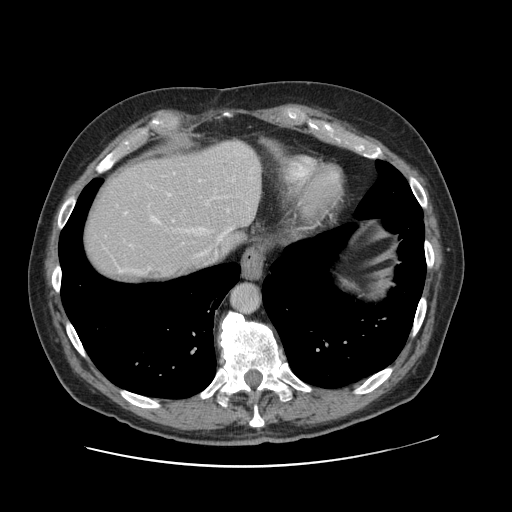
Contrast-enhanced abdominal CT, one axial slice; position 101 of 138 along the scan axis; 120 kVp; intravenous contrast given; soft-tissue window (W 400 / L 40 HU); 2.5 mm slice thickness; 512 × 512 image matrix, field of view 402 × 402 mm. Male patient, age 71 years. Case-level facts recorded for this patient, not image findings: diagnosis: colorectal cancer liver metastases, imaged before liver resection; multiple liver metastases: no; largest metastasis: 3.3 cm; disease in both lobes: no.
Annotated regions visible in this slice (expert manual segmentation):
- hepatic veins: box from (x=151, y=217) to (x=232, y=266) px
- liver: (x=83, y=141)–(x=261, y=284)
- planned liver remnant (the part of the liver to remain after resection): (x=83, y=163)–(x=225, y=284)